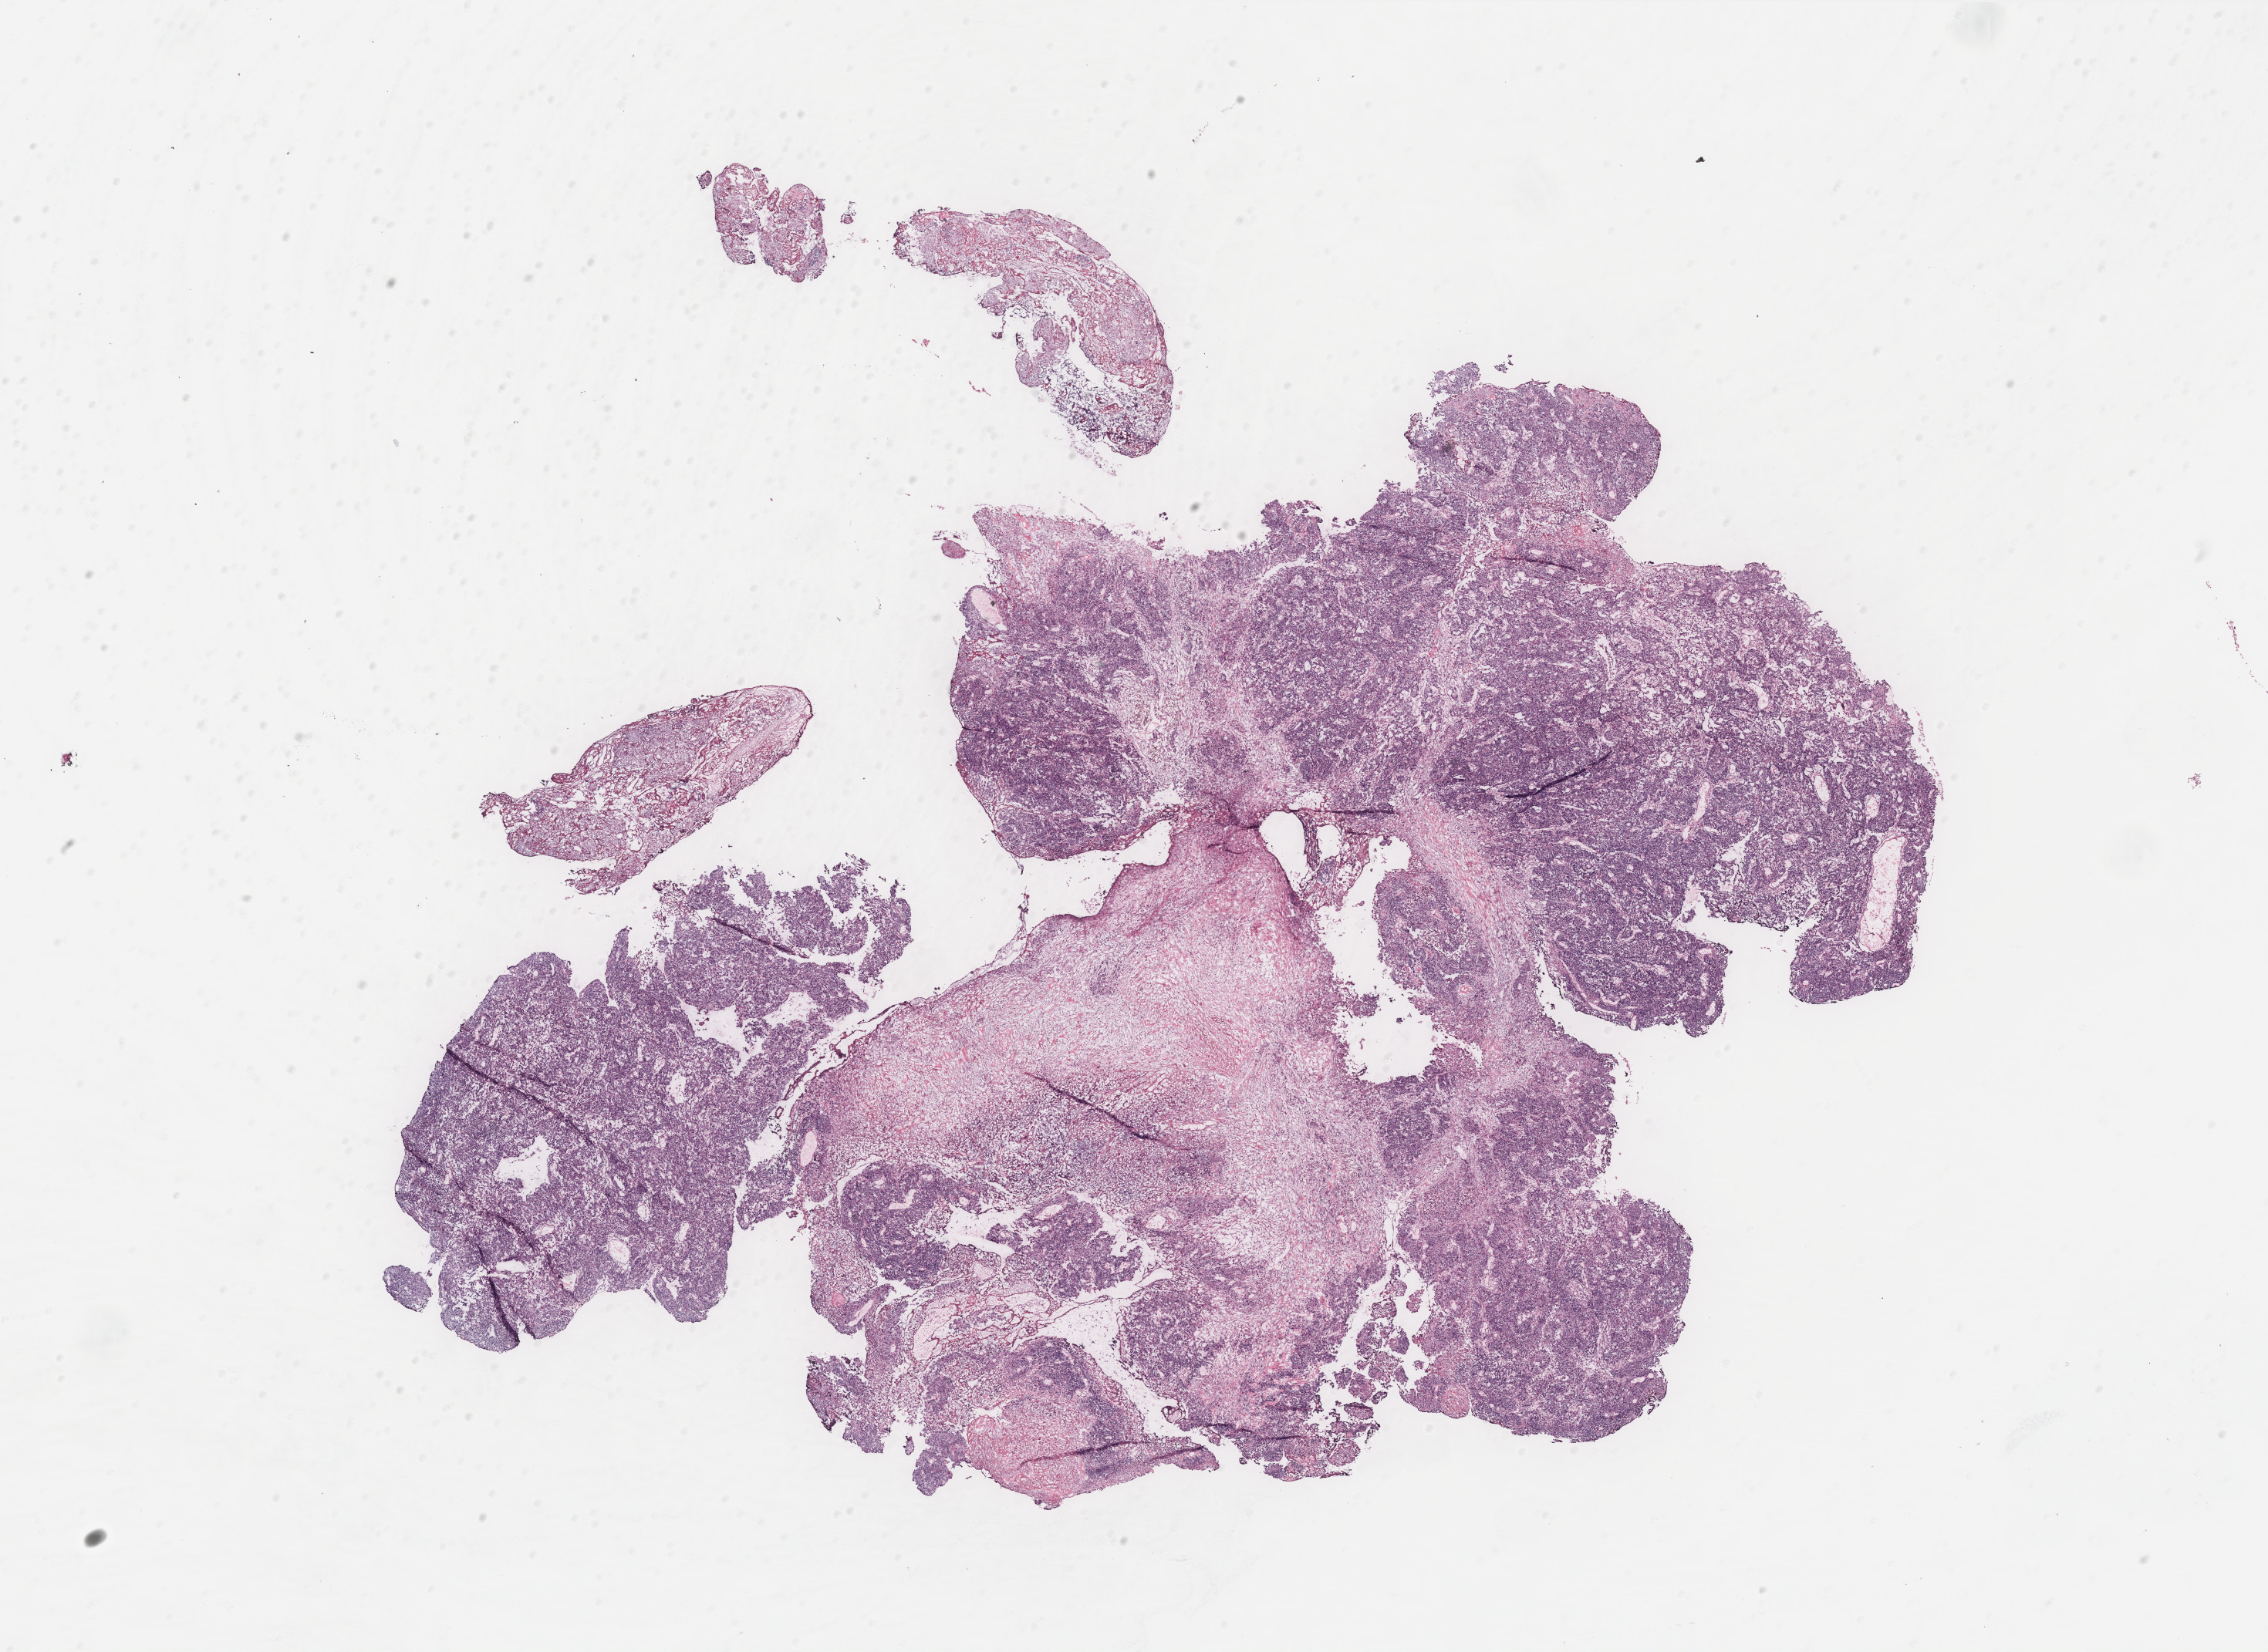
Whole-slide histology image, H&E — whole scanned area (about 23.5 x 17.1 mm, slide scanned at 40x) shown as a low-resolution overview. Ovary, tissue type not recorded. Patient sex: female.
Patient diagnosis: Serous adenocarcinoma, NOS (peritoneum, NOS).